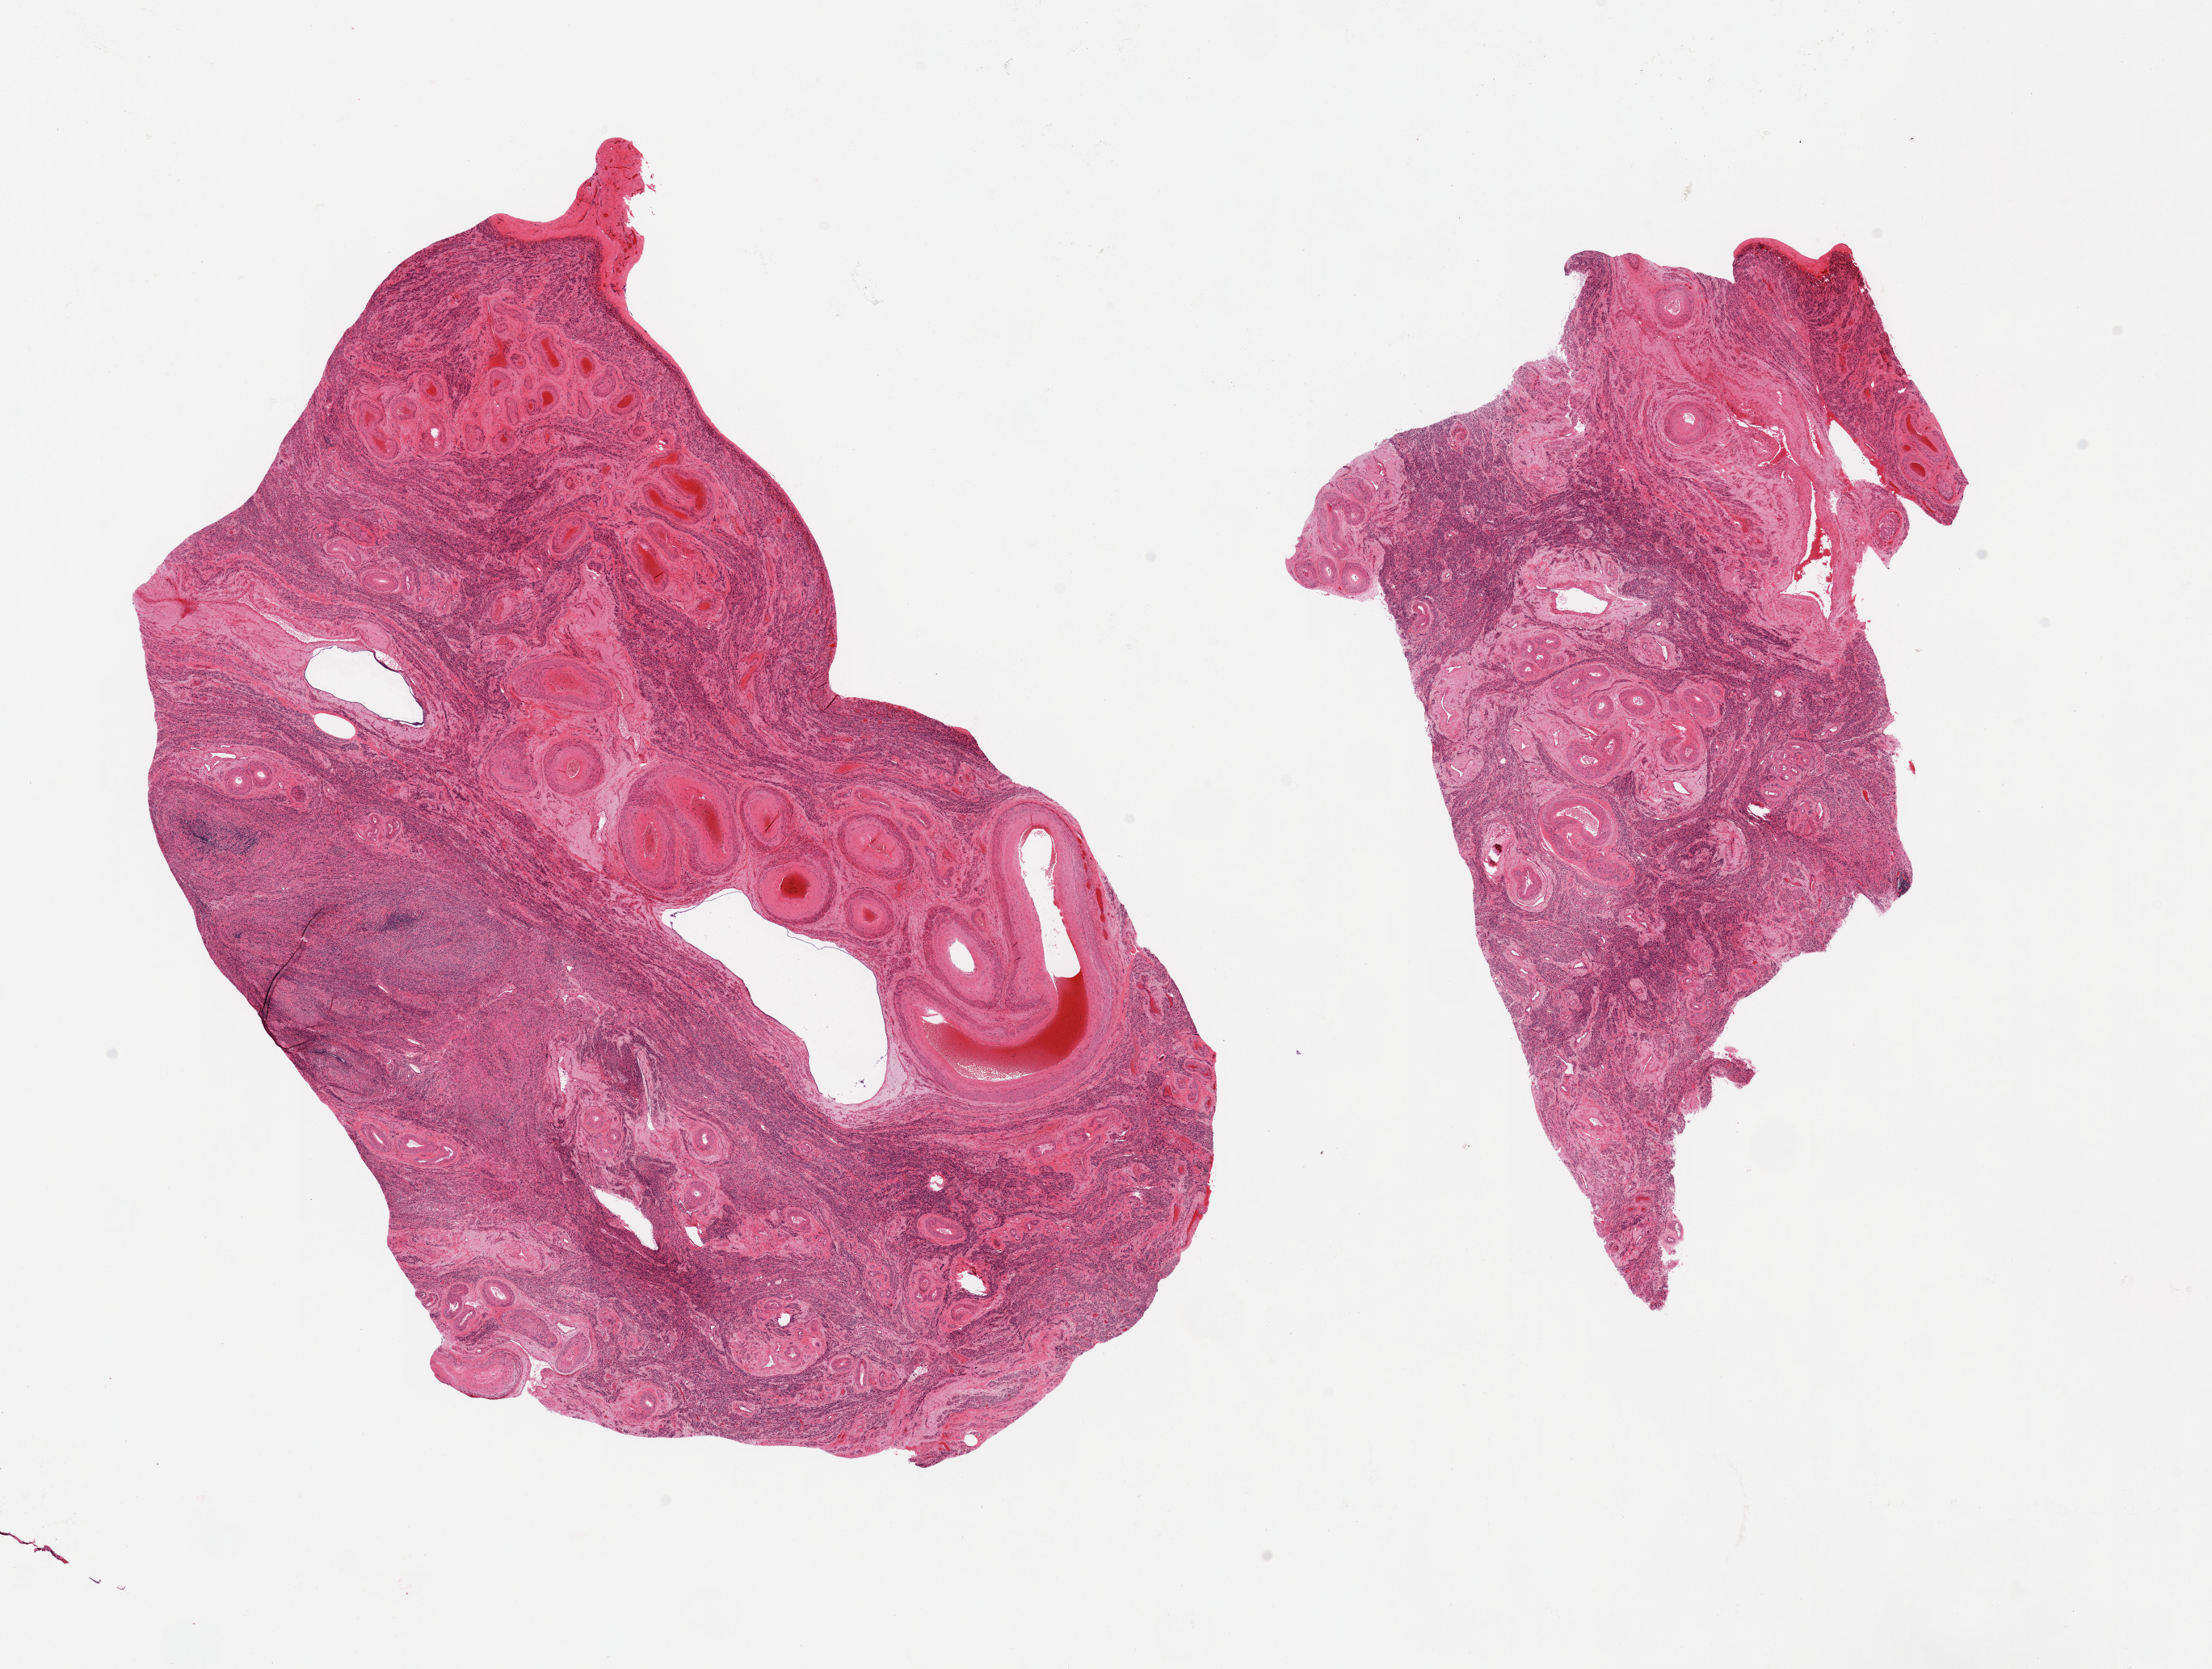
Digitized hematoxylin and eosin (H&E)-stained section, low-resolution overview of the scanned area, about 21.7 x 16.3 mm; PAXgene-fixed, paraffin-embedded tissue; sampled site (target tissue): uterus; donor tissue sample. Donor: female.
- pathologist's review note for this sample: 2 pieces; congested thick-walled vessels represent over 50% of the tissue, myometrium only in this section, few cysts (?endosalpingiosis)